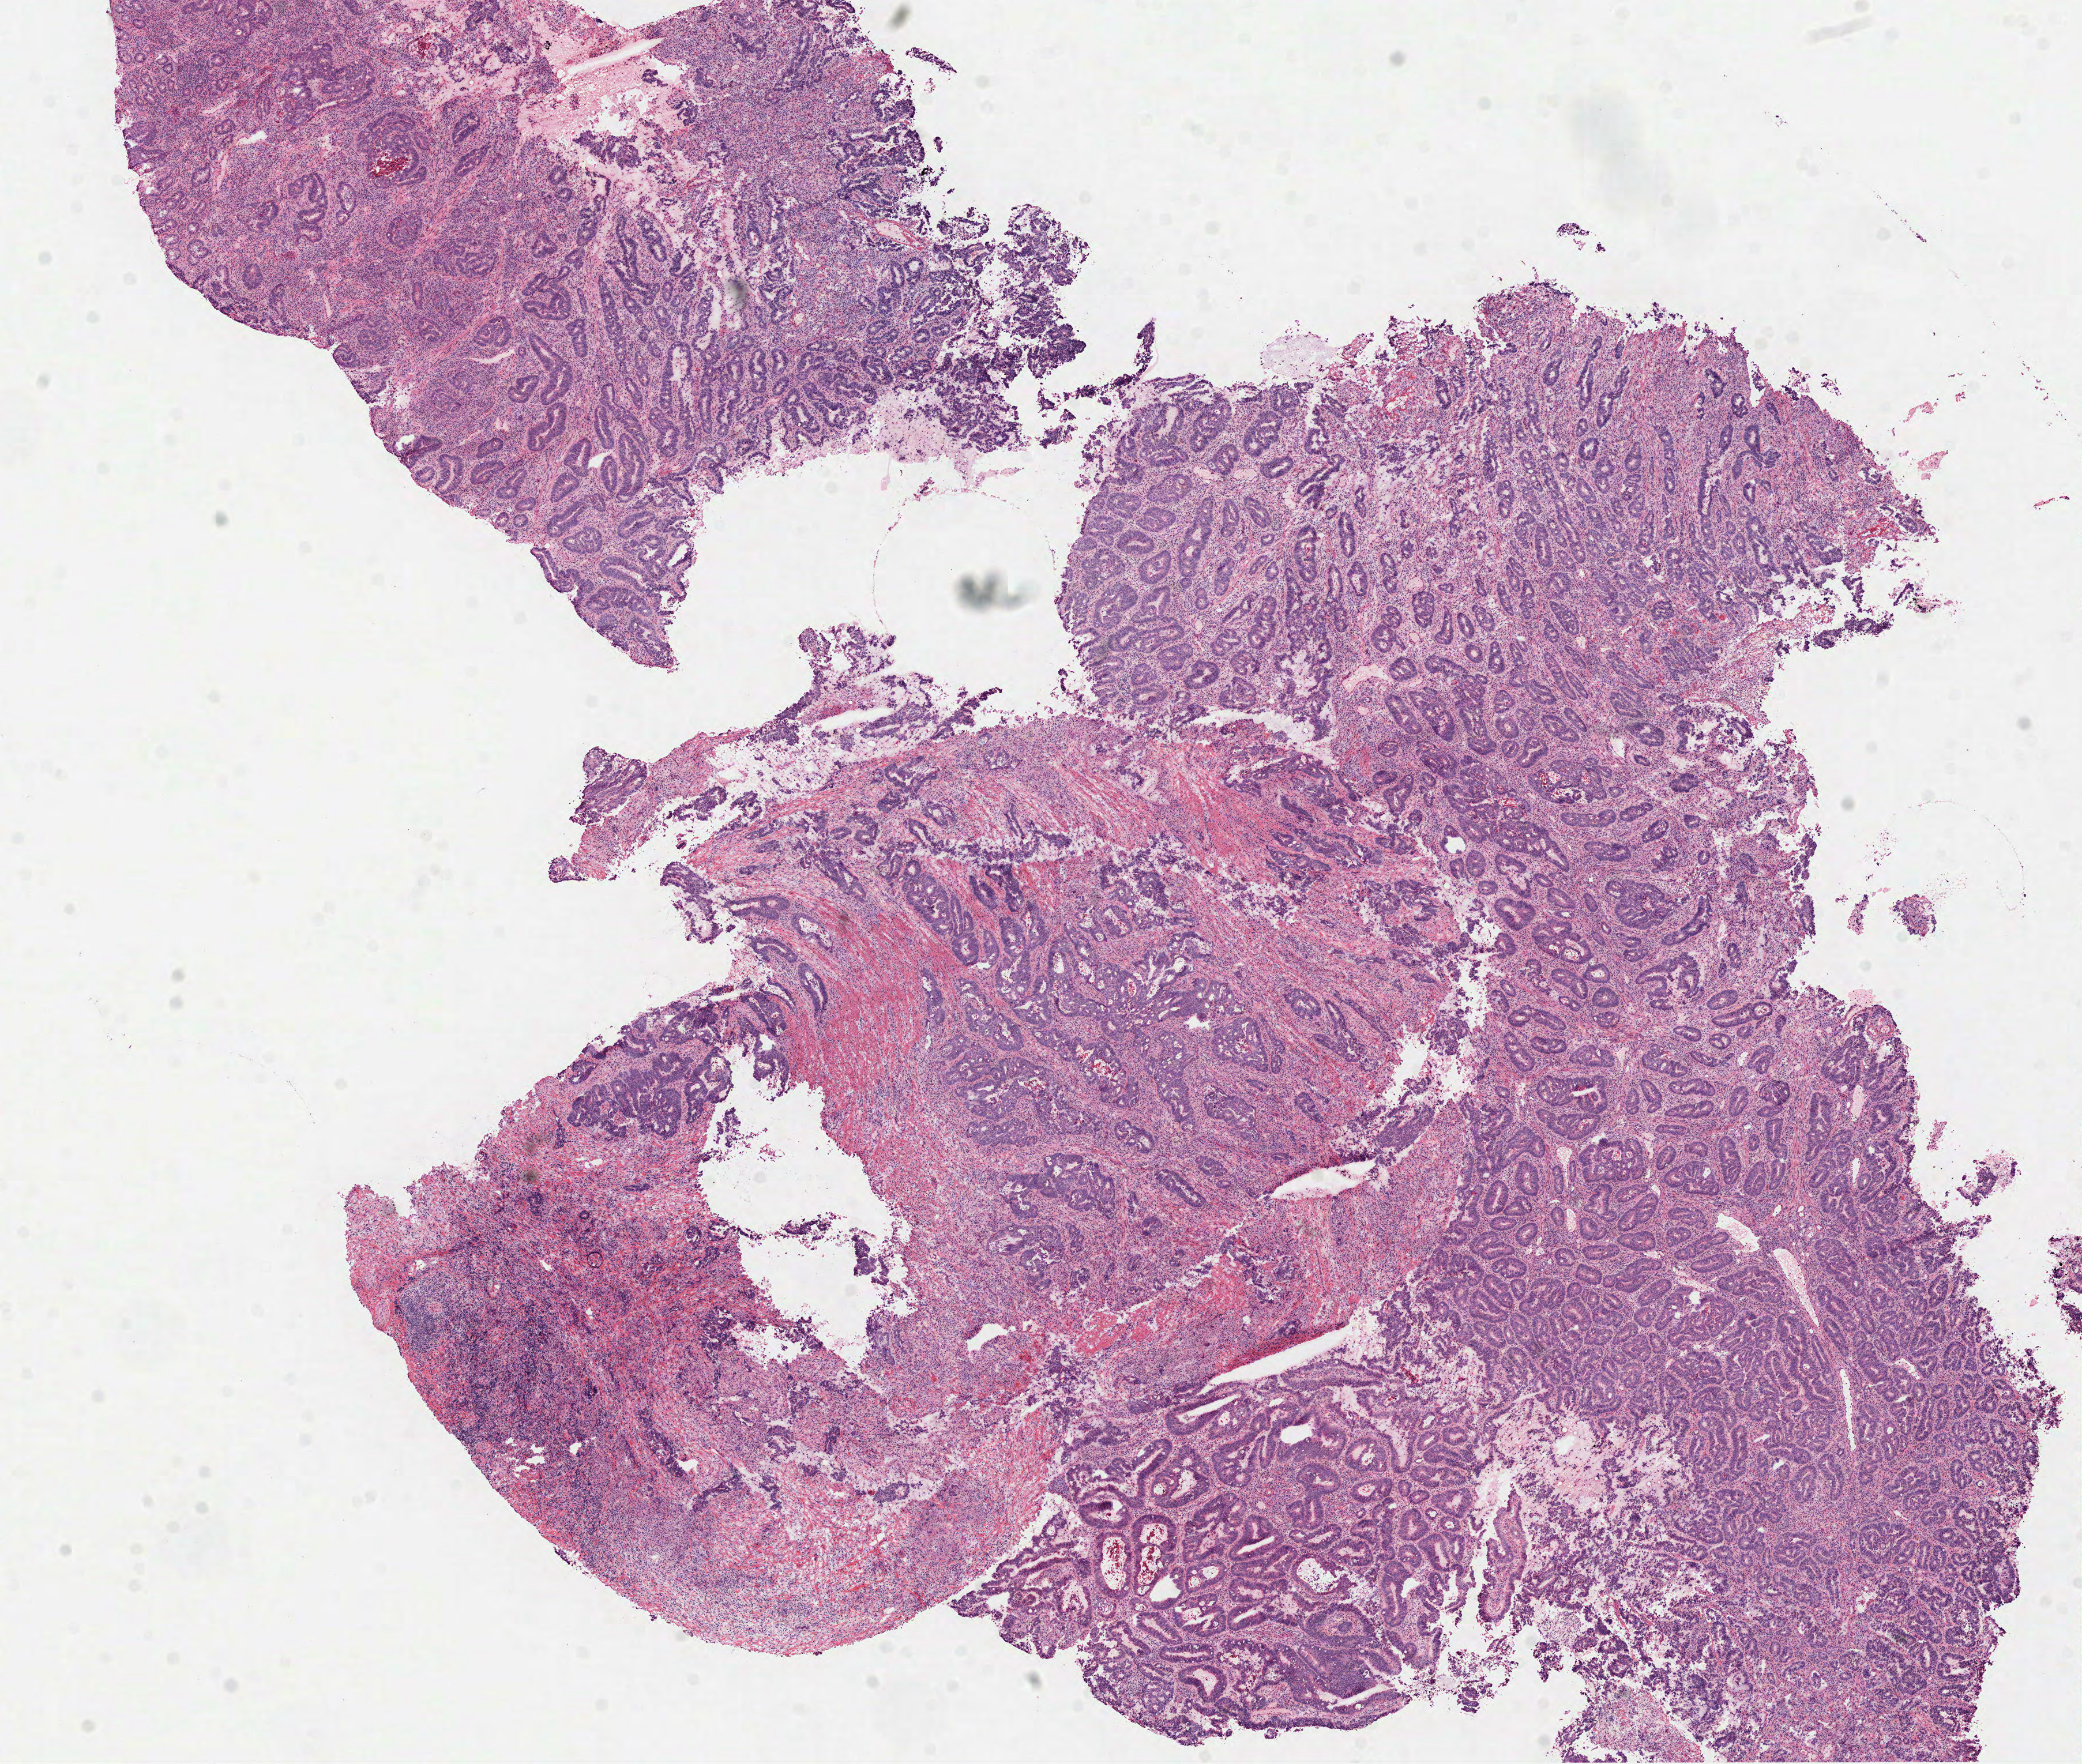
H&E whole-slide image — a low-resolution overview of the entire scanned area, about 14.6 x 12.3 mm (slide scanned at 40x); frozen section from the top of the tissue portion; sample: primary tumour, colon. Female, age 75 years at initial diagnosis. Slide review estimates, as recorded: tumour cells 70%, tumour nuclei 65%, normal cells 0%, stromal cells 20%, necrosis 10%.
• TNM: T3 N0 M0
• diagnosis: Adenocarcinoma, NOS (hepatic flexure of colon)
• AJCC pathologic stage: IIA (7th edition)